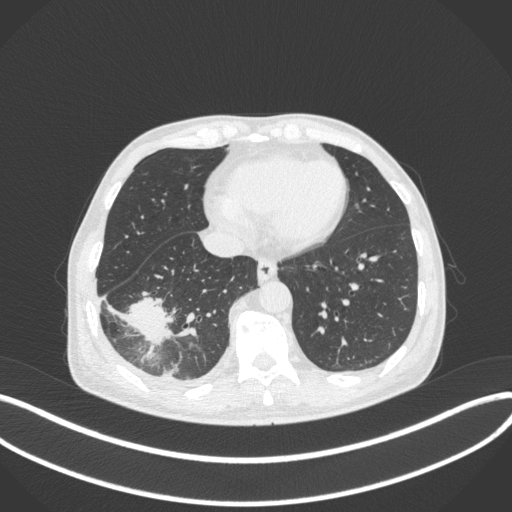
Chest CT, one axial slice. Slice 111 of 385 in the series (ordered by position). Reconstruction kernel B31f. 120 kVp. Lung window (W 1500 / L -600 HU). 512 × 512 image matrix, field of view 400 × 400 mm. Male patient, age 64 years. Case-level facts recorded for this patient, not image findings: clinical TNM (as recorded): T3 N0 M0.
Structures marked on this image (bounding box drawn by a radiologist):
- lung tumour (recorded histology: adenocarcinoma): bounding box <119,292,175,350> (left, top, right, bottom; pixels)